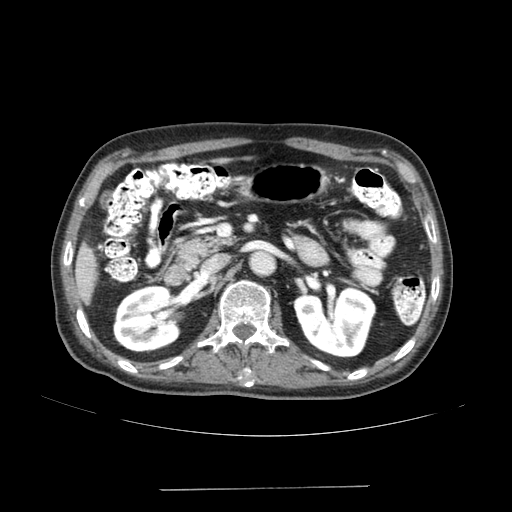
Contrast-enhanced abdominal CT (liver protocol), one axial slice; position 62 of 192 along the scan axis; 120 kVp; soft-tissue window (W 400 / L 40 HU); 512 × 512 image matrix, field of view 400 × 400 mm. Case-level facts recorded for this patient, not image findings: diagnosis: hepatocellular carcinoma (patient treated with transarterial chemoembolisation; whether this scan precedes or follows treatment is not stated here); TNM stage (as recorded): Stage-IVA; Child-Pugh class: A; tumour differentiation: poorly differentiated; tumour nodularity: uninodular.
Outlined on this slice (semi-automatic segmentation, software-assisted and operator-edited):
- liver parenchyma outside the tumour (the mass and vessels are separate outlines, so this box may not span the whole liver): bounding box <74,243,97,304> (left, top, right, bottom; pixels)